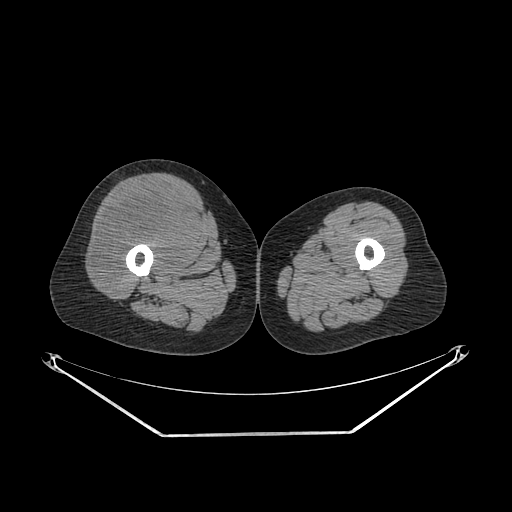
CT of an extremity soft-tissue mass (from a PET/CT study), one axial slice; position 244 of 311 along the scan axis; soft-tissue window (W 400 / L 40 HU); 3.75 mm slice thickness; 512 × 512 image matrix, field of view 500 × 500 mm. Female patient. Case-level facts recorded for this patient, not image findings: histological type: pleiomorphic undifferentiated sarcoma; grade: high; site of the primary tumour: right quadricep.
Outlined on this slice (expert contour drawn on MRI and transferred to this co-registered scan by the dataset authors):
- tumour plus oedema (research contour): box from (x=96, y=189) to (x=195, y=284) px
- tumour (research contour): (x=96, y=189)–(x=195, y=284)